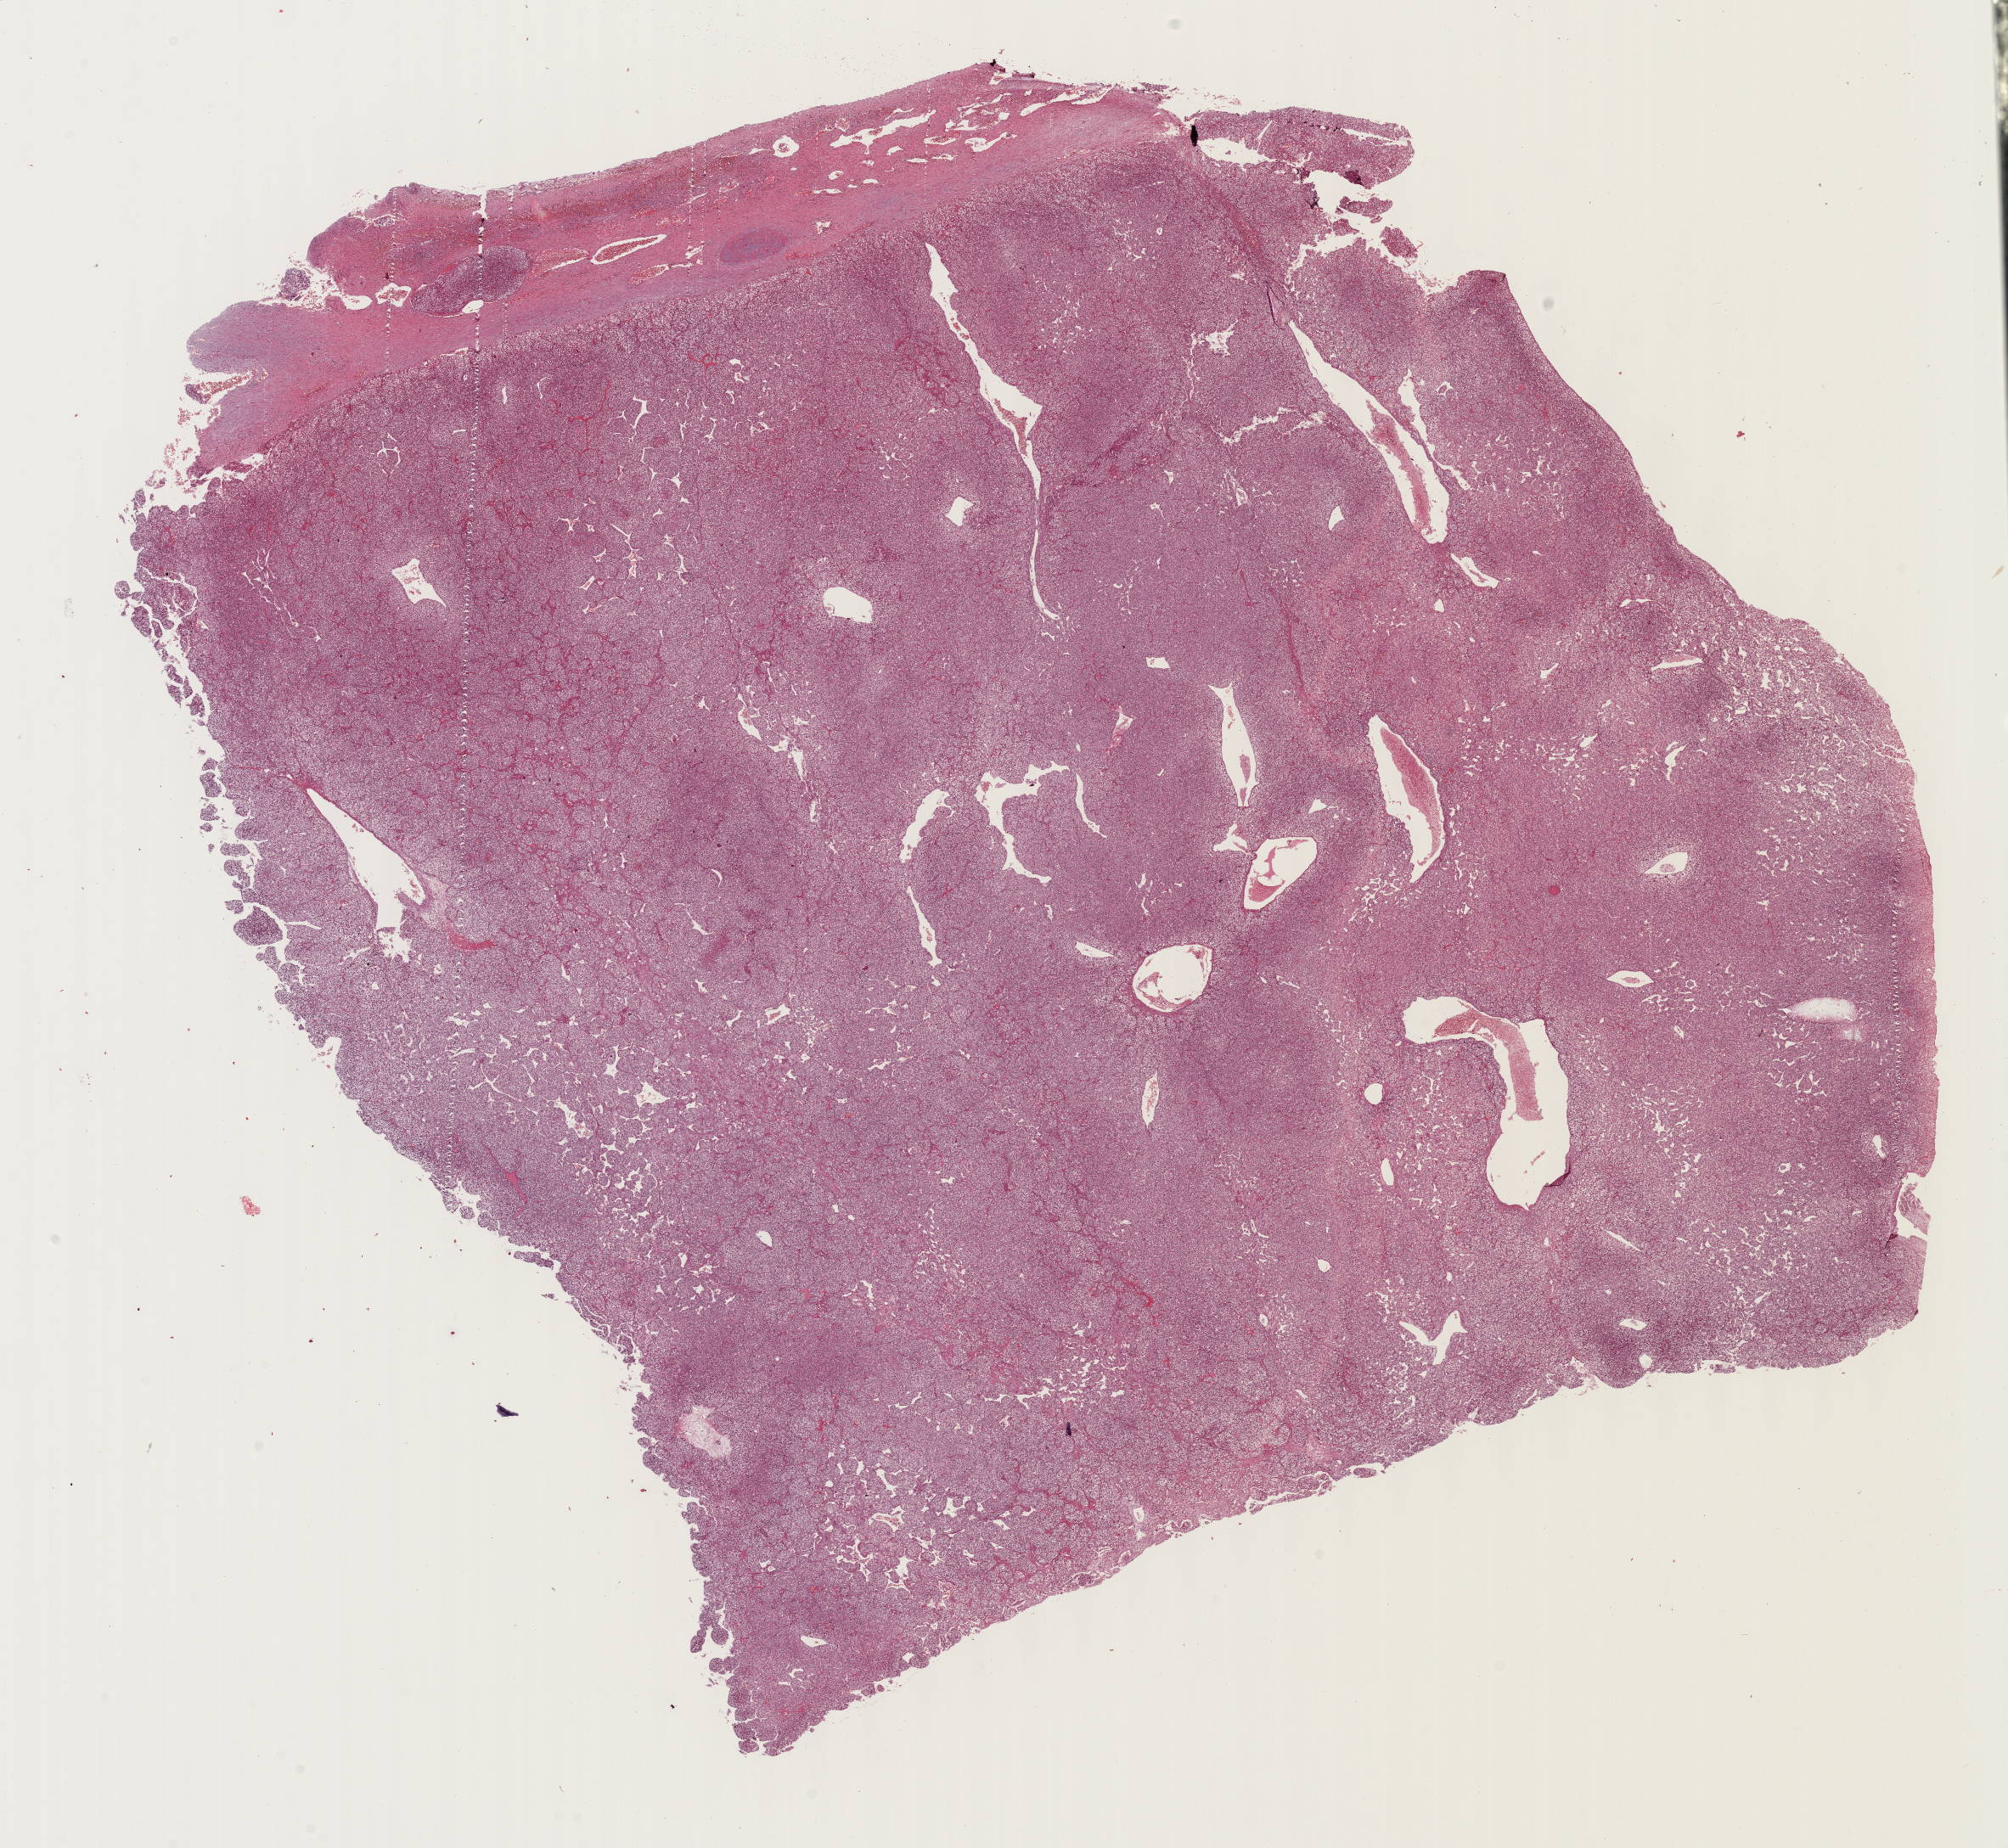
Digitized H&E tissue section (whole slide) — shown as a low-resolution overview of the whole scanned area (about 19.1 x 17.6 mm, acquisition: 40x scan), formalin-fixed paraffin-embedded (FFPE) diagnostic section, liver, primary tumour sample. Male, age 18 years at initial diagnosis. Histologic grade: G1 (well differentiated).
• pathologic diagnosis: Hepatocellular carcinoma, NOS
• AJCC pathologic stage: IIIC (6th edition)